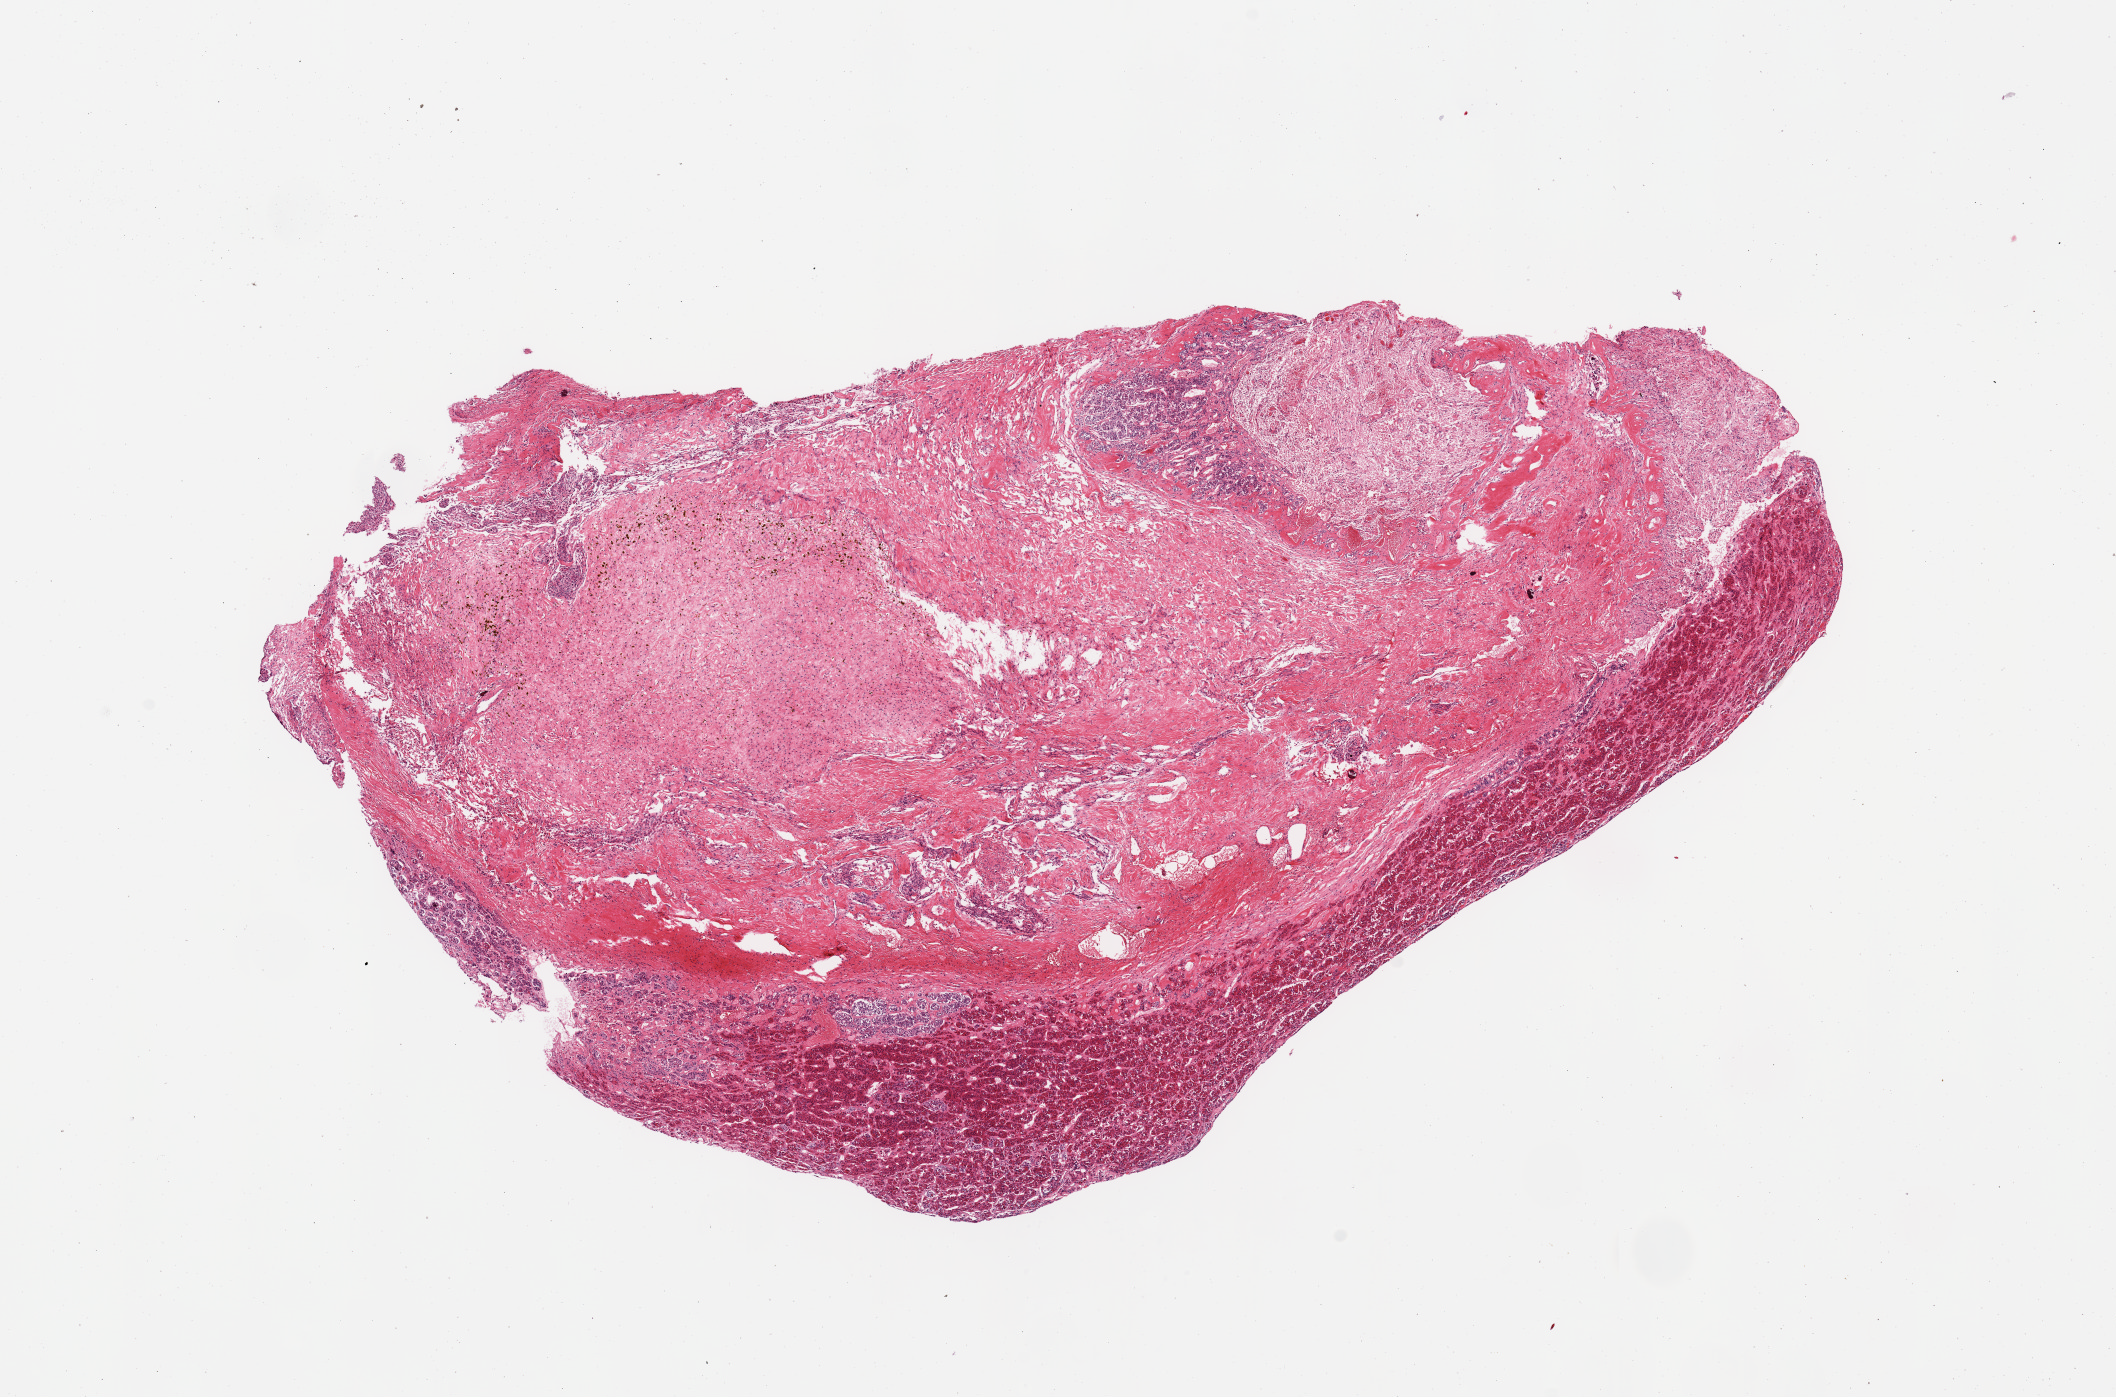
Digitized hematoxylin and eosin (H&E)-stained section, whole scanned area (about 16.7 x 11.0 mm, slide scanned at 20x) shown as a low-resolution overview, PAXgene-fixed, paraffin-embedded tissue, sampled site (target tissue): pituitary, donor tissue sample. Donor sex: male.
Pathologist's review note for this sample: 1 piece: thin rim of adenohypophysis with large central core of neurohypophysis.